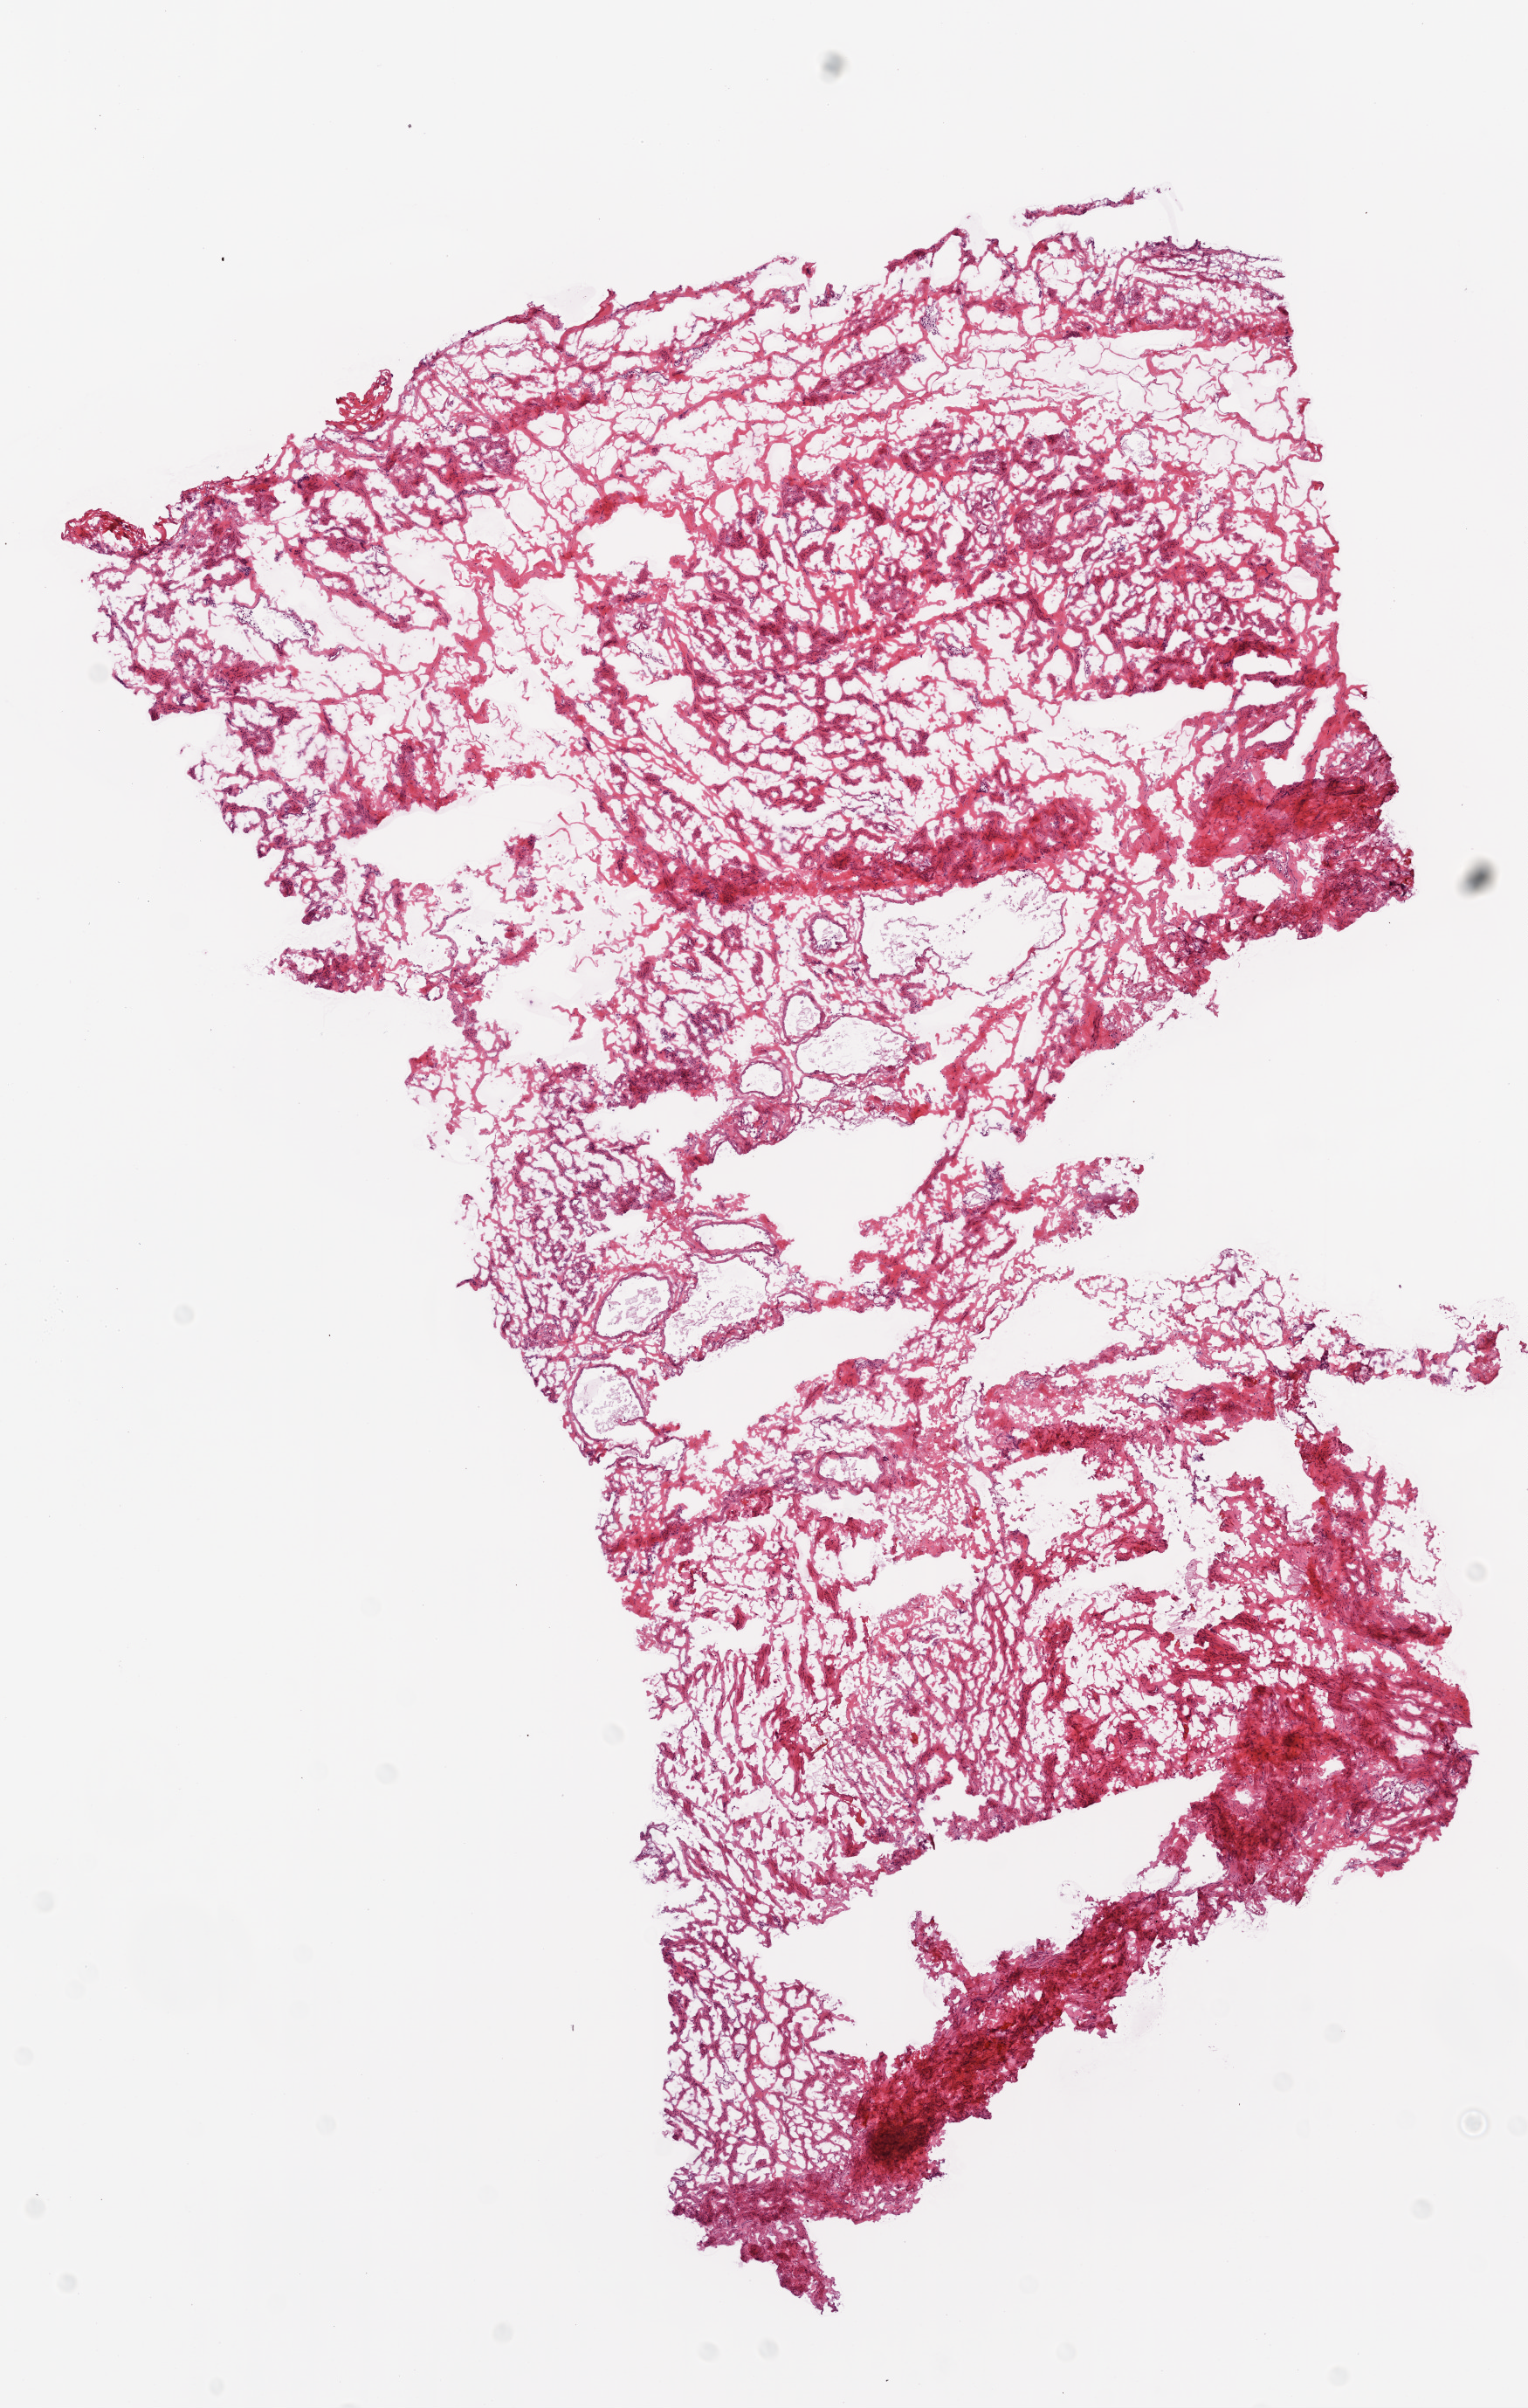
Whole-slide histology image, H&E, whole scanned area (about 7.0 x 11.1 mm, acquisition: 20x scan) shown as a low-resolution overview. Frozen section. Ovary, solid tissue normal (non-tumour tissue) sample. Female patient; age at initial diagnosis 54 years.
- this section: solid tissue normal sample (biorepository sample class)
- patient diagnosis: Serous cystadenocarcinoma, NOS